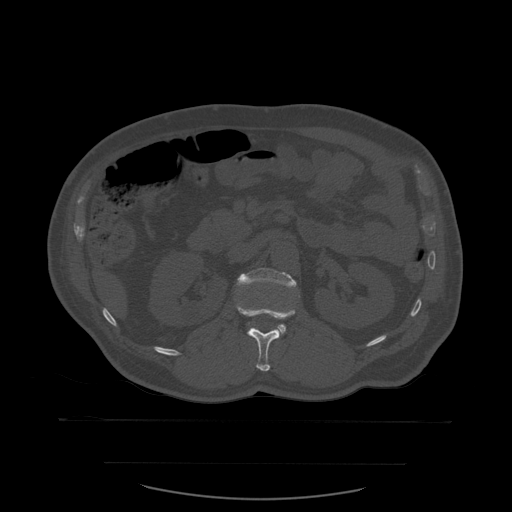
CT including the spine, one axial slice. Position 237 of 590 along the scan axis. Bone window (W 1800 / L 400 HU). 1.25 mm slice thickness. 512 × 512 image matrix. Patient age 71 years. Case-level facts recorded for this patient, not image findings: primary cancer: lung.
Annotated regions visible in this slice (semi-automatically segmented with operator editing):
- L1 vertebra: box from (x=236, y=302) to (x=296, y=372) px
- L2 vertebra: (x=237, y=268)–(x=297, y=335)